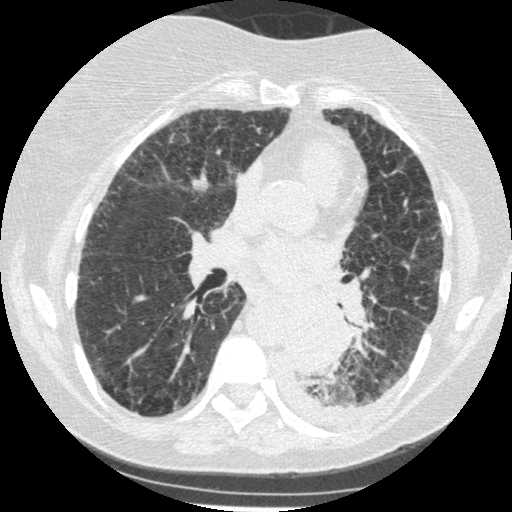
Chest CT (low-dose screening protocol), one axial image, third screening round (two years after baseline), lung window (W 1500 / L -600 HU), 1.25 mm slice thickness, slice 216 of 341 in the series. Female, age 60 years at enrolment. Former smoker at enrolment.
Lesion marked by an expert reader, bounding box [x1, y1, x2, y2] px = [273, 305, 342, 374]. Screening reader's record for this exam (one nodule recorded; not confirmed to be the boxed lesion): non-calcified nodule or mass ≥4 mm, left lower lobe, 54 × 38 mm, smooth margins, soft tissue attenuation, pre-existing on the prior screen: yes; interval growth: yes. Official screen result: positive, other.